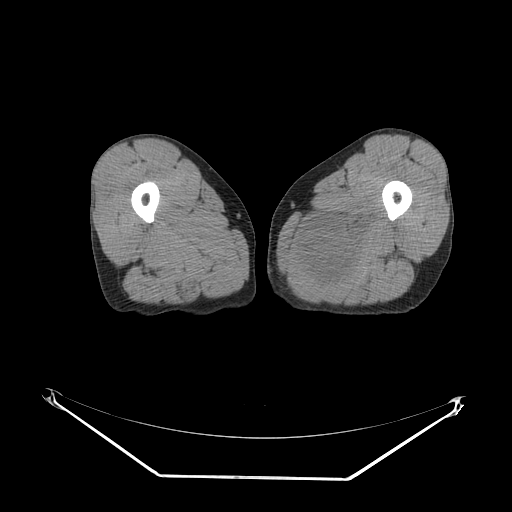
CT of an extremity soft-tissue mass (from a PET/CT study), one axial slice; position 17 of 267 along the scan axis; 140 kVp; soft-tissue window (W 400 / L 40 HU); 3.75 mm slice thickness; 512 × 512 image matrix. Male patient. Case-level facts recorded for this patient, not image findings: histological type: pleiomorphic liposarcoma; grade: high; site of the primary tumour: left thigh.
Annotated regions visible in this slice (expert contour drawn on MRI and transferred to this co-registered scan by the dataset authors):
- gross tumour volume including surrounding oedema: box from (x=301, y=206) to (x=380, y=291) px
- gross tumour volume (mass): (x=306, y=233)–(x=362, y=286)